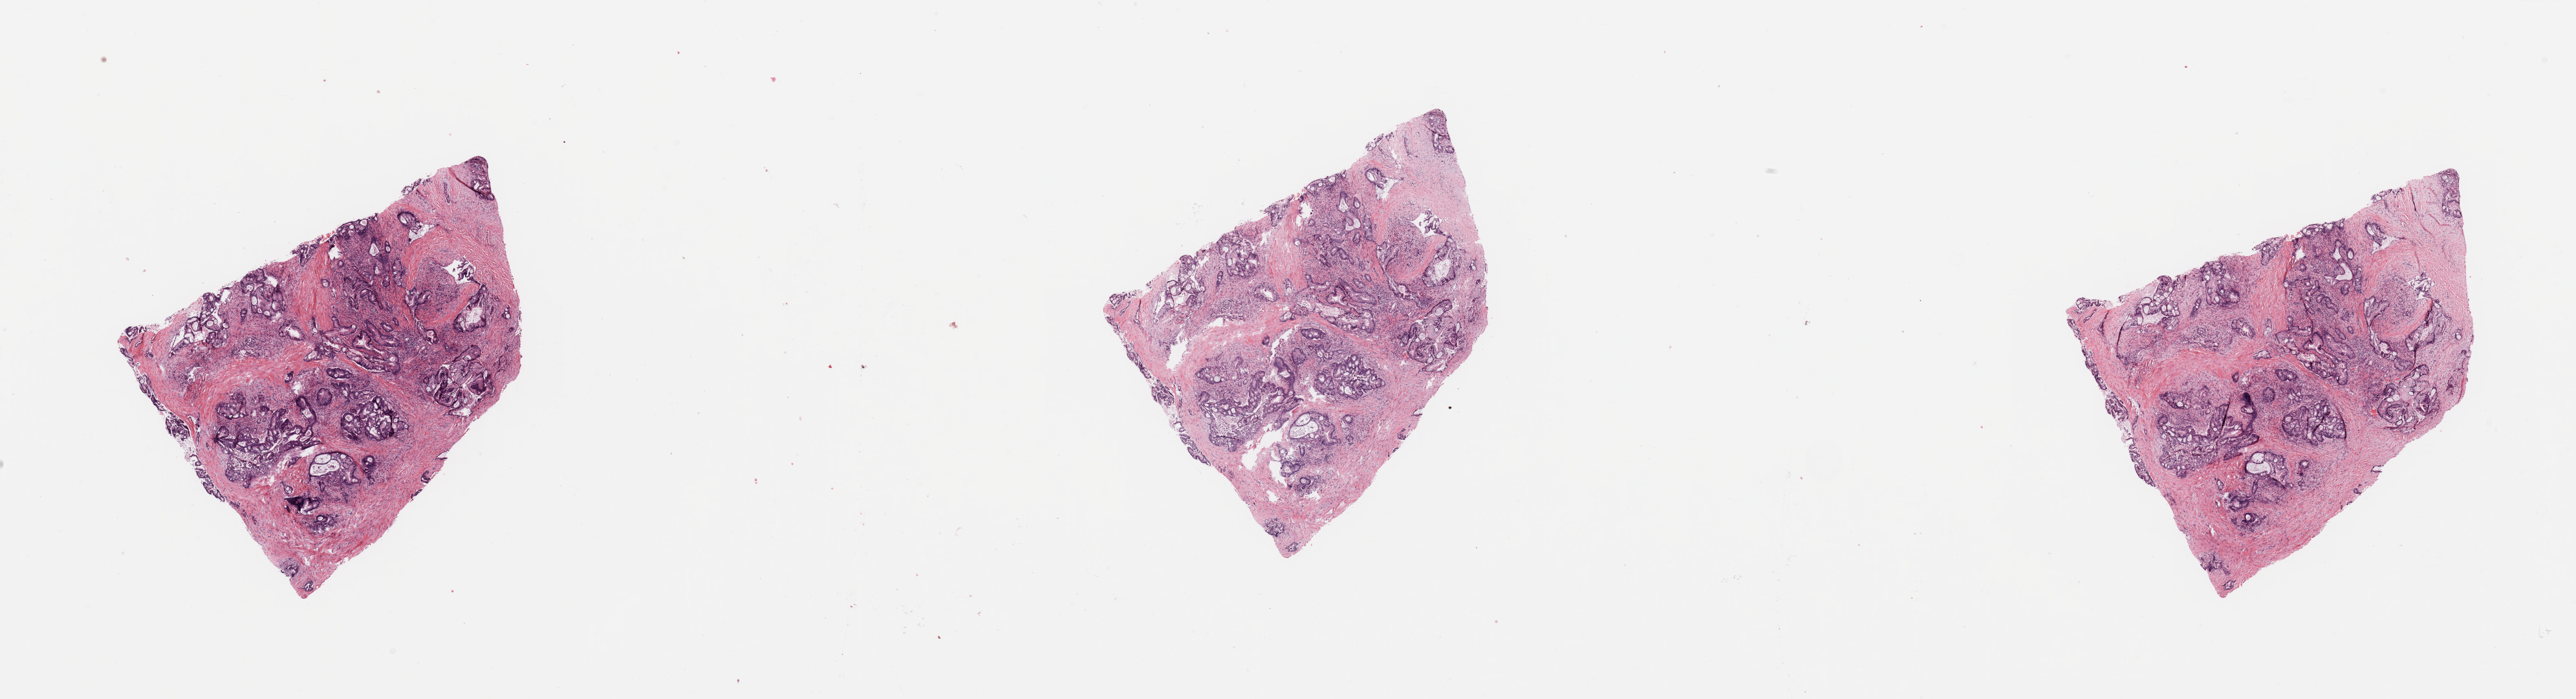
Digitized H&E tissue section (whole slide), a low-resolution overview of the entire scanned area, about 31.5 x 8.5 mm. Tumour tissue sample, sampled site: pancreas. 34-year-old female patient. Histologic grade: G2 (moderately differentiated). Slide review estimates, as recorded: tumour nuclei 80%, necrosis 0%.
• AJCC pathologic stage: IIB
• primary tumour site (as recorded): head
• histologic diagnosis: Infiltrating duct carcinoma, NOS